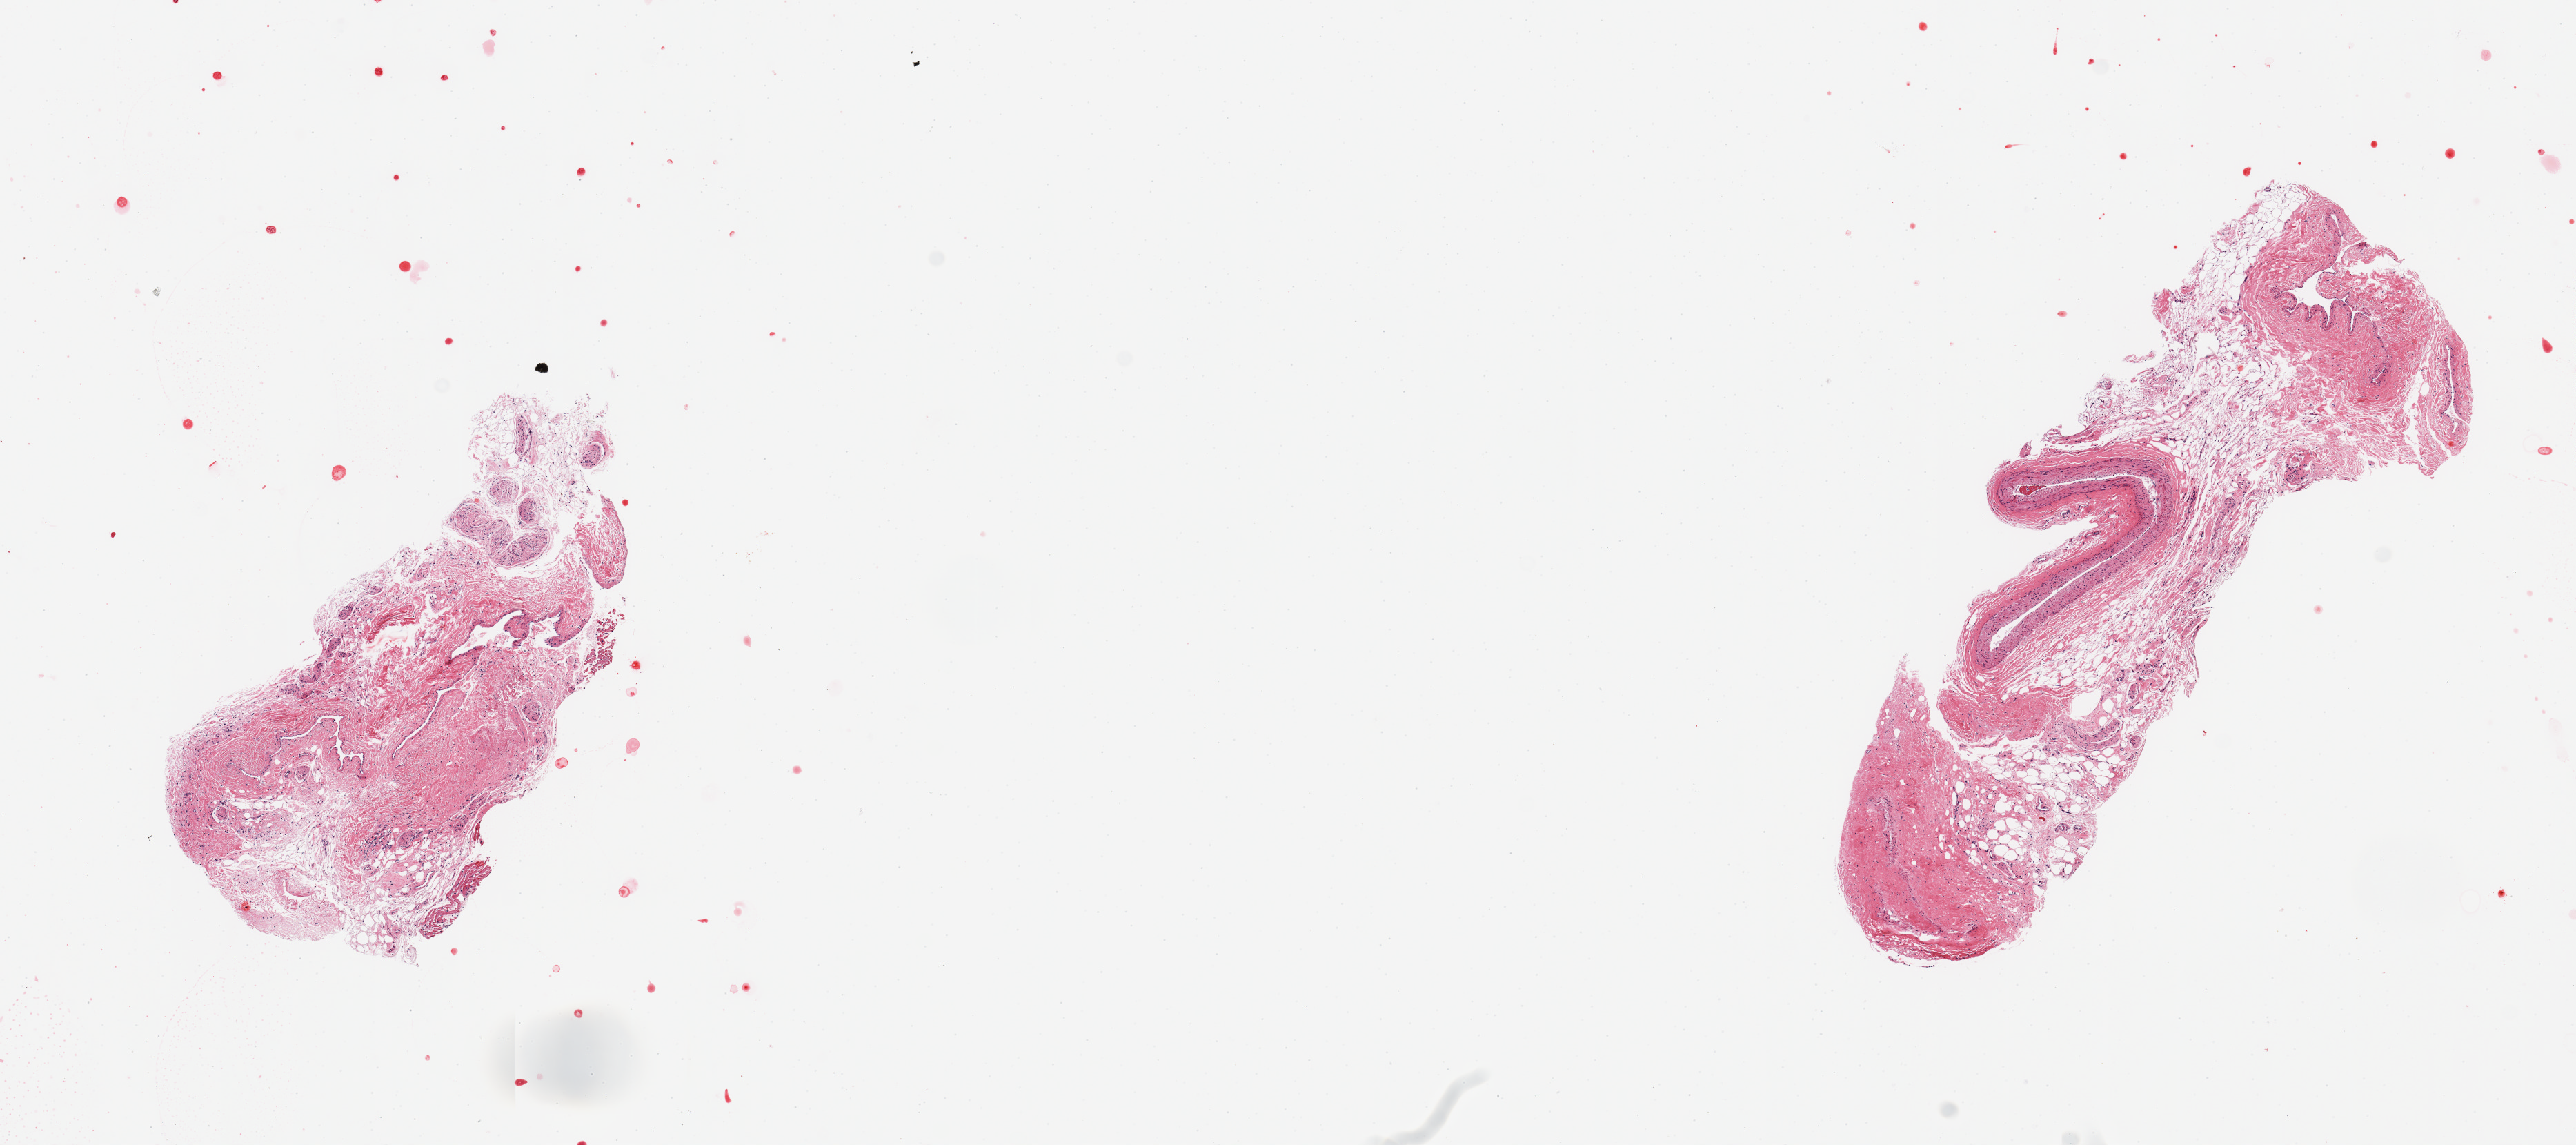
H&E whole-slide image, brightfield, a low-resolution overview of the entire scanned area, about 14.8 x 6.6 mm (from a 20x scan), PAXgene-fixed, paraffin-embedded tissue, section of coronary artery (target tissue), donor tissue sample. Donor: female.
Reviewer comment on this tissue sample: 2 pieces; artery represents ~10-15% of 1 piece, rest is extraneous tissues (fibrous/fat/vein/nerve).